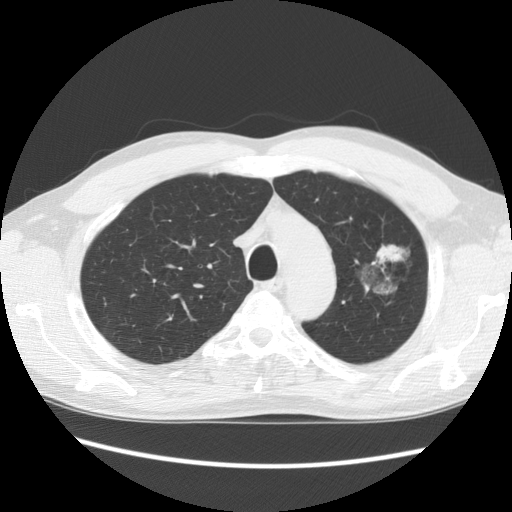
Axial slice from a low-dose chest CT screening exam; second screening round (one year after baseline); lung window (W 1500 / L -600 HU); 2.5 mm slice thickness; 512 × 512 image matrix. Male, age 61 years at enrolment.
Expert-annotated lung lesion, bounding box <344,223,426,301> (left, top, right, bottom; pixels). The exam's reader record, not a measurement of the box and not confirmed to be the same lesion: non-calcified nodule or mass ≥4 mm, left upper lobe, 34 × 32 mm, poorly defined margins, mixed attenuation, pre-existing on the prior screen: yes; interval growth: no. Later outcome: lung cancer diagnosed 704 days after this screen (after the third annual screen) — bronchiolo-alveolar adenocarcinoma, NOS, left upper lobe, well differentiated (G1), stage IB (AJCC 6th edition), 44 mm at pathology.